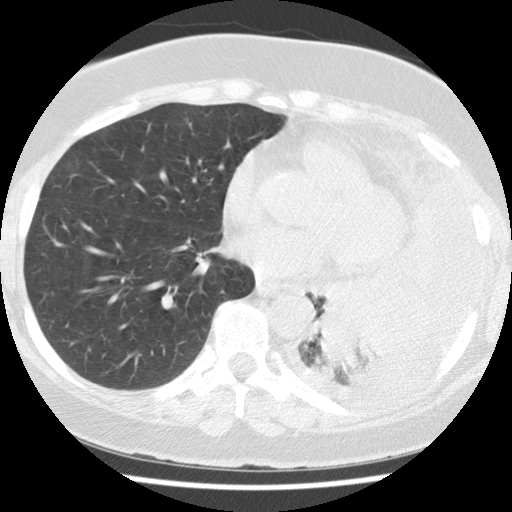
Axial slice from a low-dose chest CT screening exam; baseline annual screen; lung window (W 1500 / L -600 HU); 2.5 mm slice thickness; 120 kVp; slice 68 of 114 in the series. Female participant, aged 65 years at enrolment. Current smoker at enrolment.
• Expert-annotated lung lesion, bounding box <312,282,431,382> (left, top, right, bottom; pixels).
• The exam's reader record, not a measurement of the box and not confirmed to be the same lesion: non-calcified nodule or mass ≥4 mm, left lower lobe, 74 × 48 mm, spiculated (stellate) margins, soft tissue attenuation.
• Later outcome: lung cancer diagnosed 13 days after this screen — adenocarcinoma, NOS, left lower lobe, stage IV (AJCC 6th edition), 74 mm at pathology.